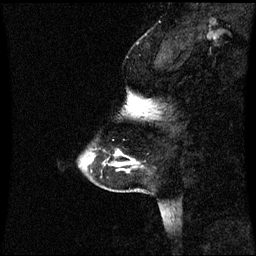
Breast MRI (dynamic contrast-enhanced), one sagittal slice; position 11 of 60 along the scan axis; dynamic contrast-enhanced series, image 2 of 3 at this slice position (ordered by acquisition); 1.5 T; TE 4.2 ms, TR 8.9 ms; 256 × 256 image matrix, field of view 220 × 220 mm. Patient: female, 43 years. Case-level facts recorded for this patient, not image findings: setting: breast cancer imaged before/during neoadjuvant chemotherapy; receptor status: HR-positive, HER2-negative.
Outlined on this slice (semi-automatically segmented with operator editing):
- analysis volume of interest (the breast-tissue region the enhancement analysis was run in; not a lesion): box from (x=84, y=116) to (x=144, y=171) px
- tumour enhancement mask (voxels above the 70 % enhancement threshold inside the analysis volume of interest): (x=116, y=152)–(x=122, y=155)